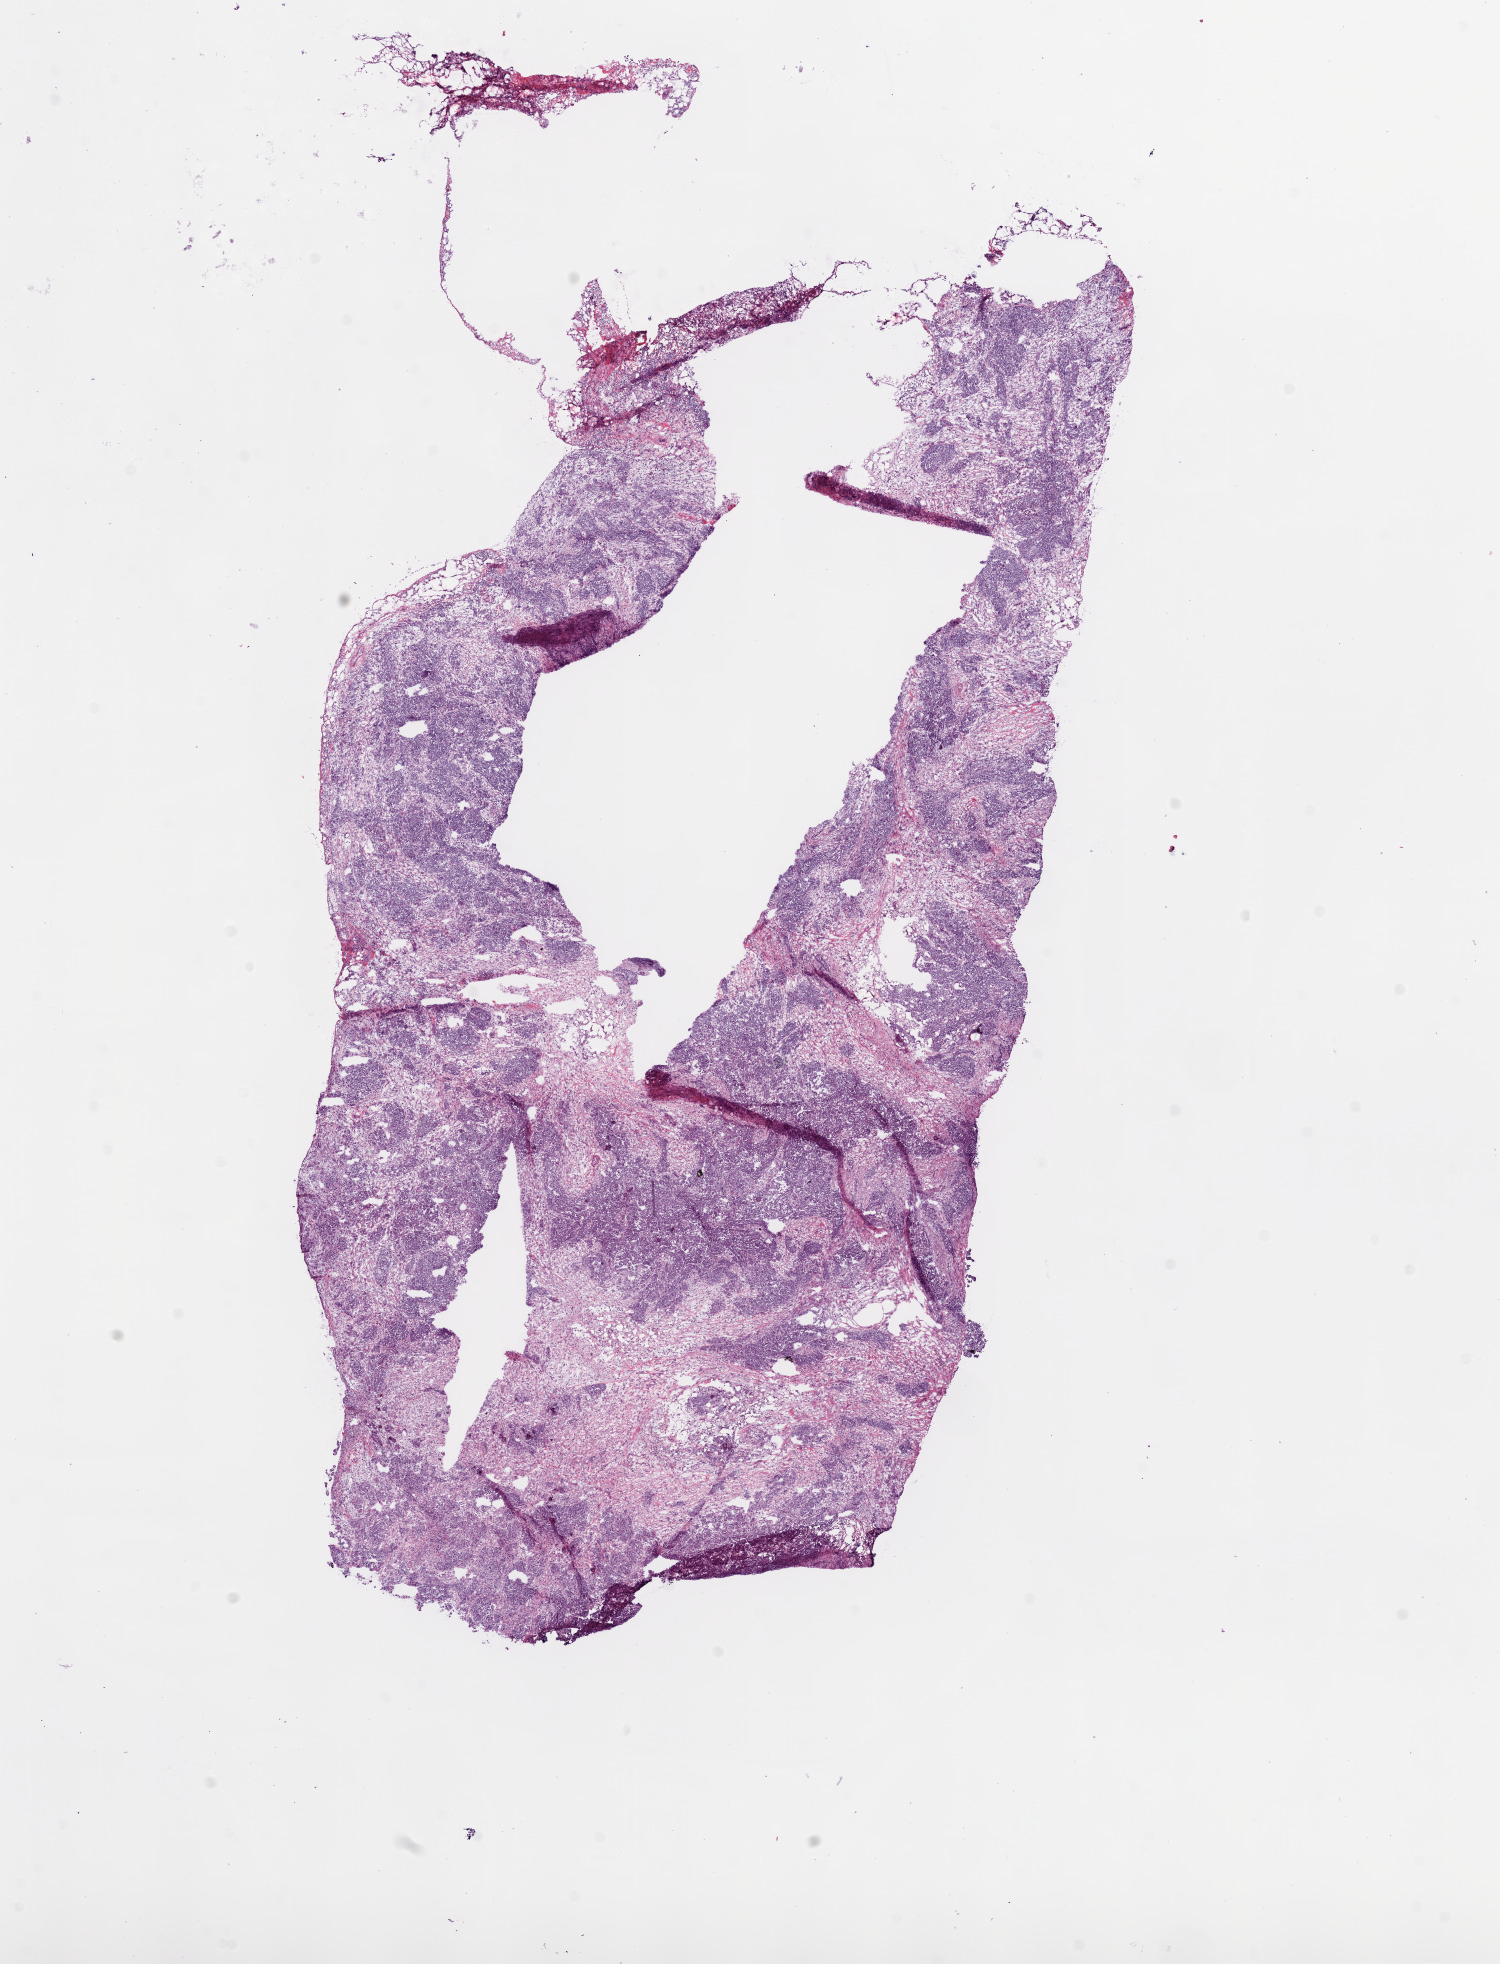
Whole-slide histology image, H&E-stained — shown as a low-resolution overview of the whole scanned area (about 12.0 x 15.8 mm, slide scanned at 20x), frozen section, primary tumour sample from the ovary. Female patient; age at initial diagnosis 71 years. Histologic grade: G3 (poorly differentiated). Composition of this section per pathologist review: tumour cells 55%, tumour nuclei 75%, normal cells 0%, stromal cells 40%, necrosis 5%.
Pathologic diagnosis: Serous cystadenocarcinoma, NOS. FIGO stage: IIIC. Laterality: bilateral.